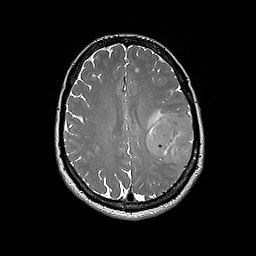
Brain MRI from a brain-tumour surgery series, one axial slice; position 75 of 192 along the scan axis; 256 × 256 image matrix, field of view 250 × 250 mm. Case-level facts recorded for this patient, not image findings: histopathology: Glioblastoma; WHO grade: 4.
Structures marked on this image (outlined manually by an expert reader):
- tumour: bounding box <146,113,194,164> (left, top, right, bottom; pixels)